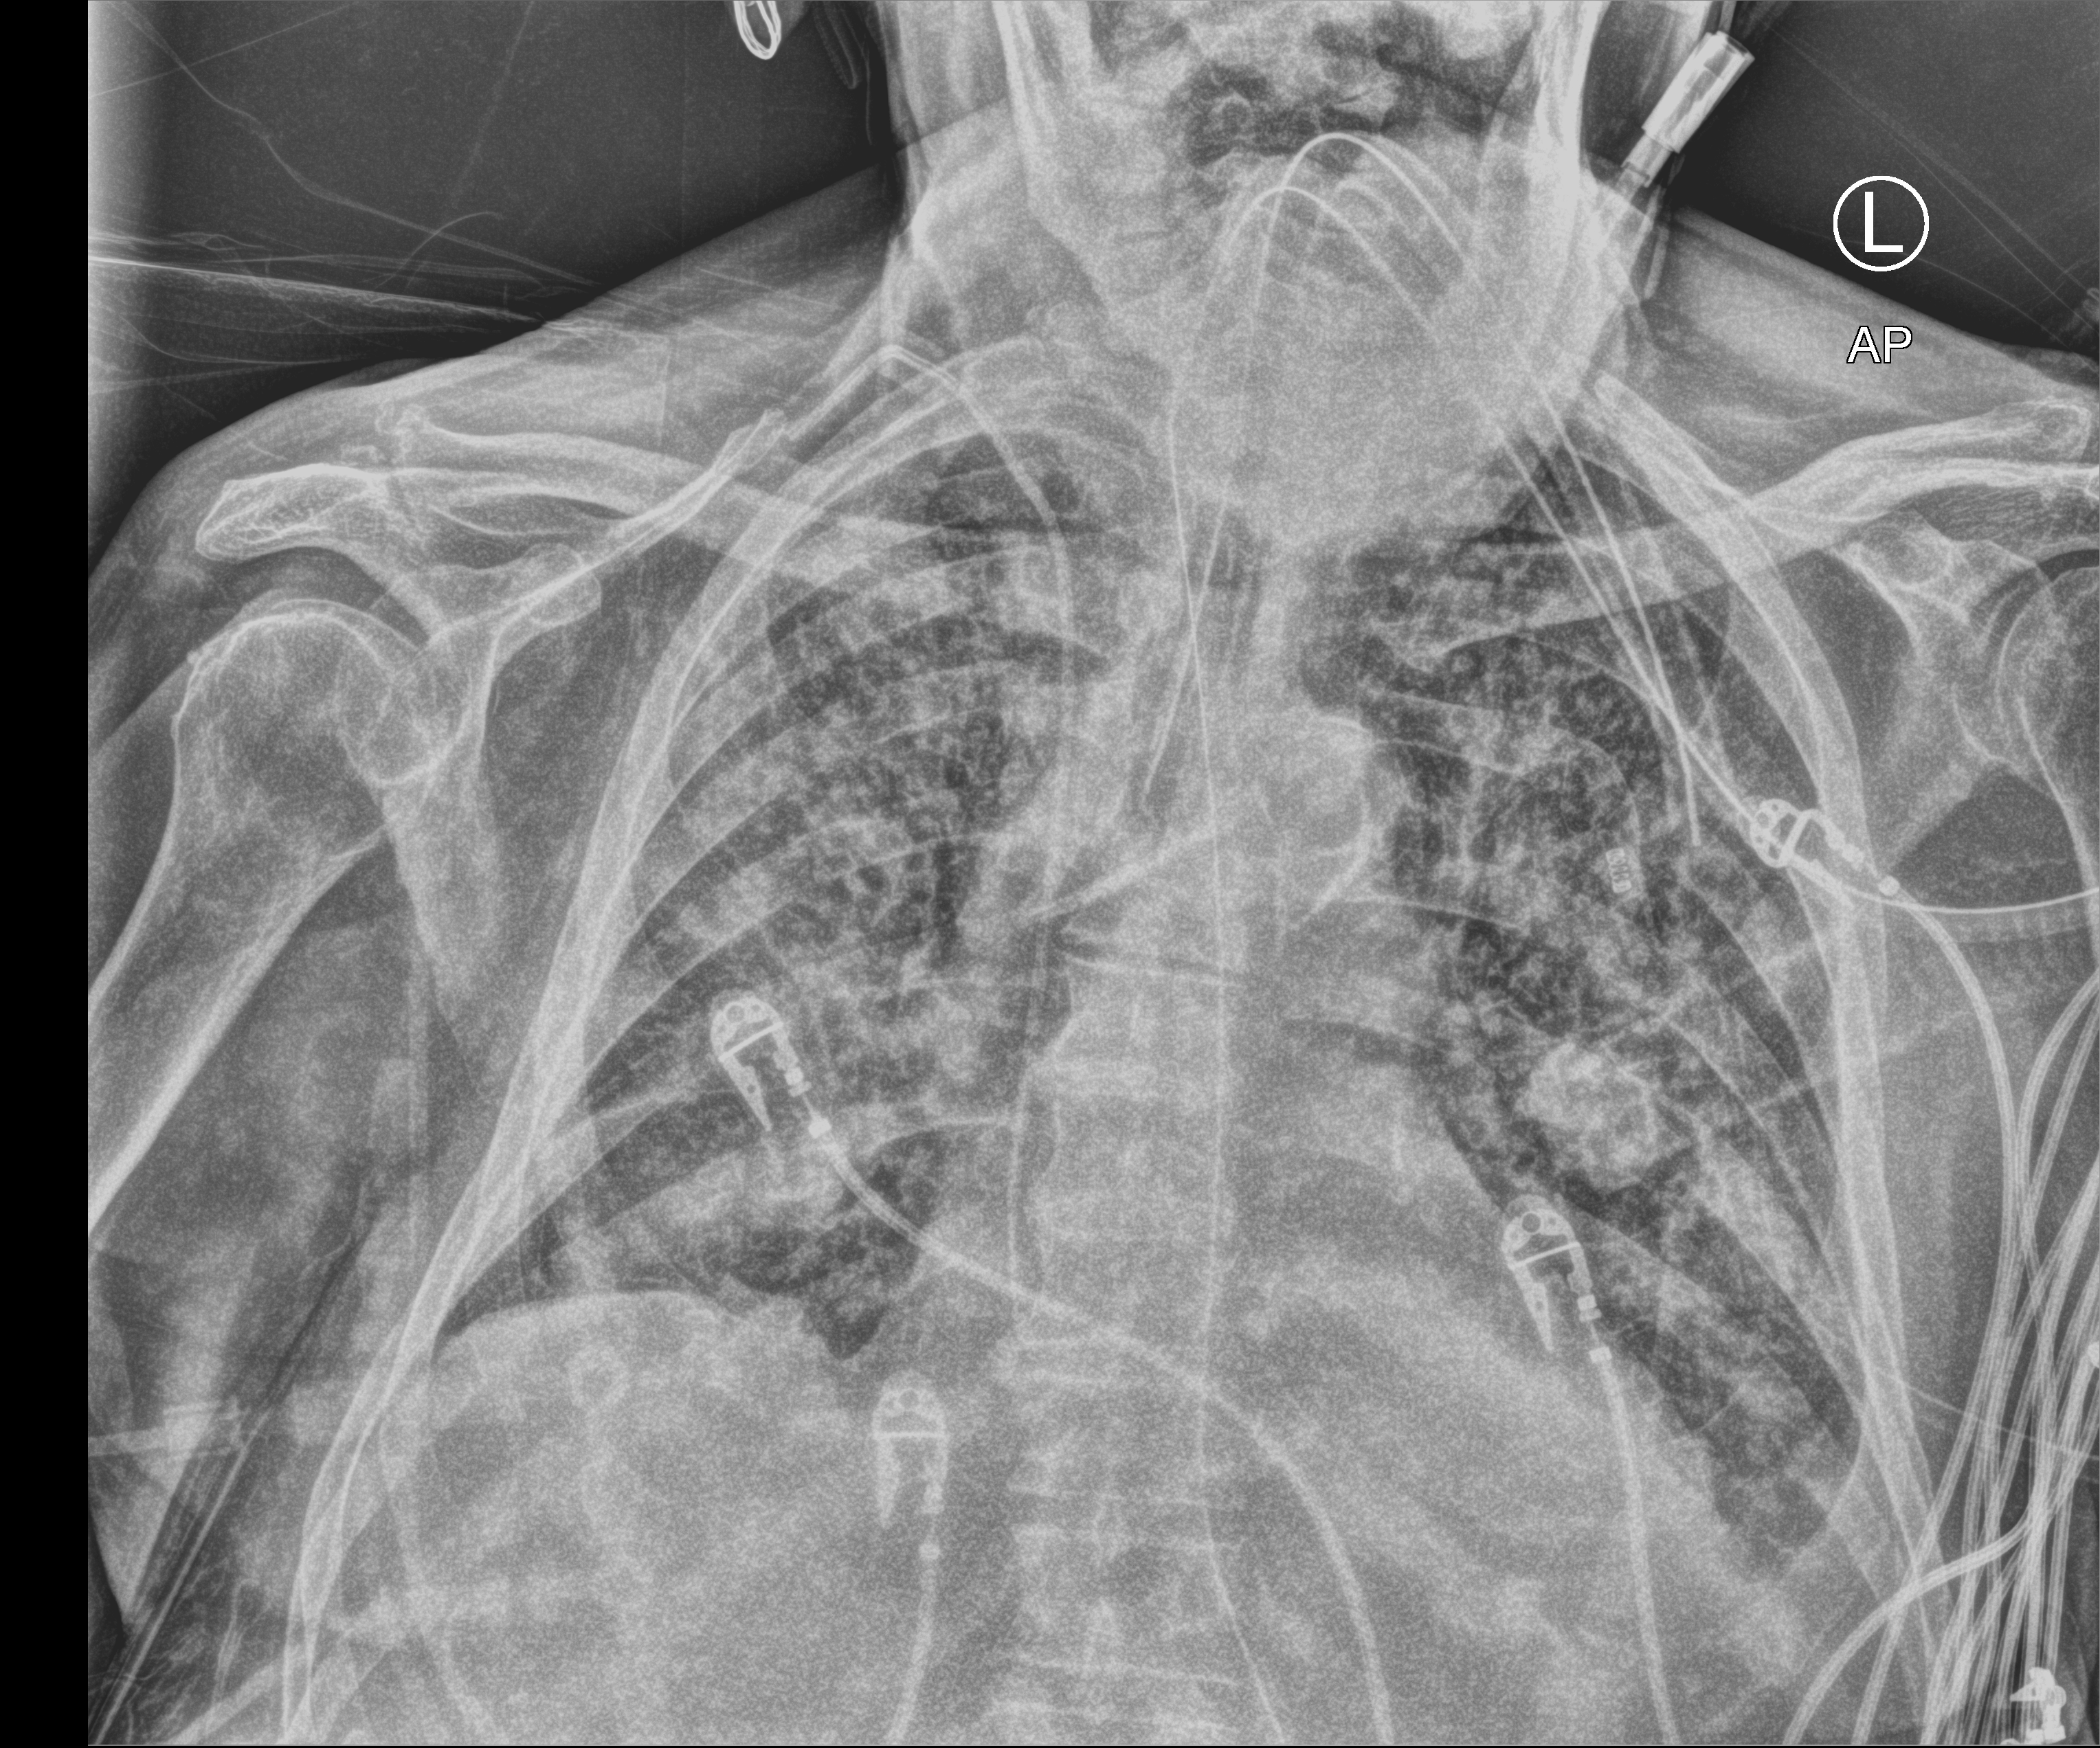
Portable chest radiograph, anteroposterior (AP) projection. Patient hospitalised with COVID-19; male, aged 75–90 years.
Admission-level facts for this patient (not findings on this image; timing relative to this image not recorded): length of hospital stay: 28 days; admitted to intensive care during this hospital stay: yes.